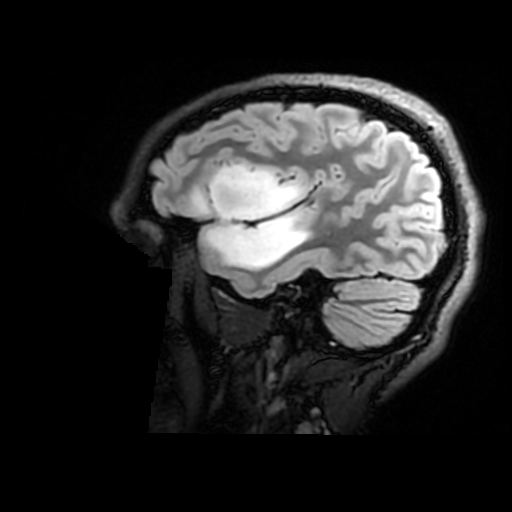
Brain MRI from a brain-tumour surgery series, one sagittal slice. Position 131 of 176 along the scan axis. T2 FLAIR. 1 mm slice thickness. 512 × 512 image matrix, field of view 240 × 240 mm. Case-level facts recorded for this patient, not image findings: histopathology: Astrocytoma; WHO grade: 2; IDH mutation: yes; tumour location: Right Insular.
Outlined on this slice (expert manual segmentation):
- tumour: bounding box <197,164,309,271> (left, top, right, bottom; pixels)